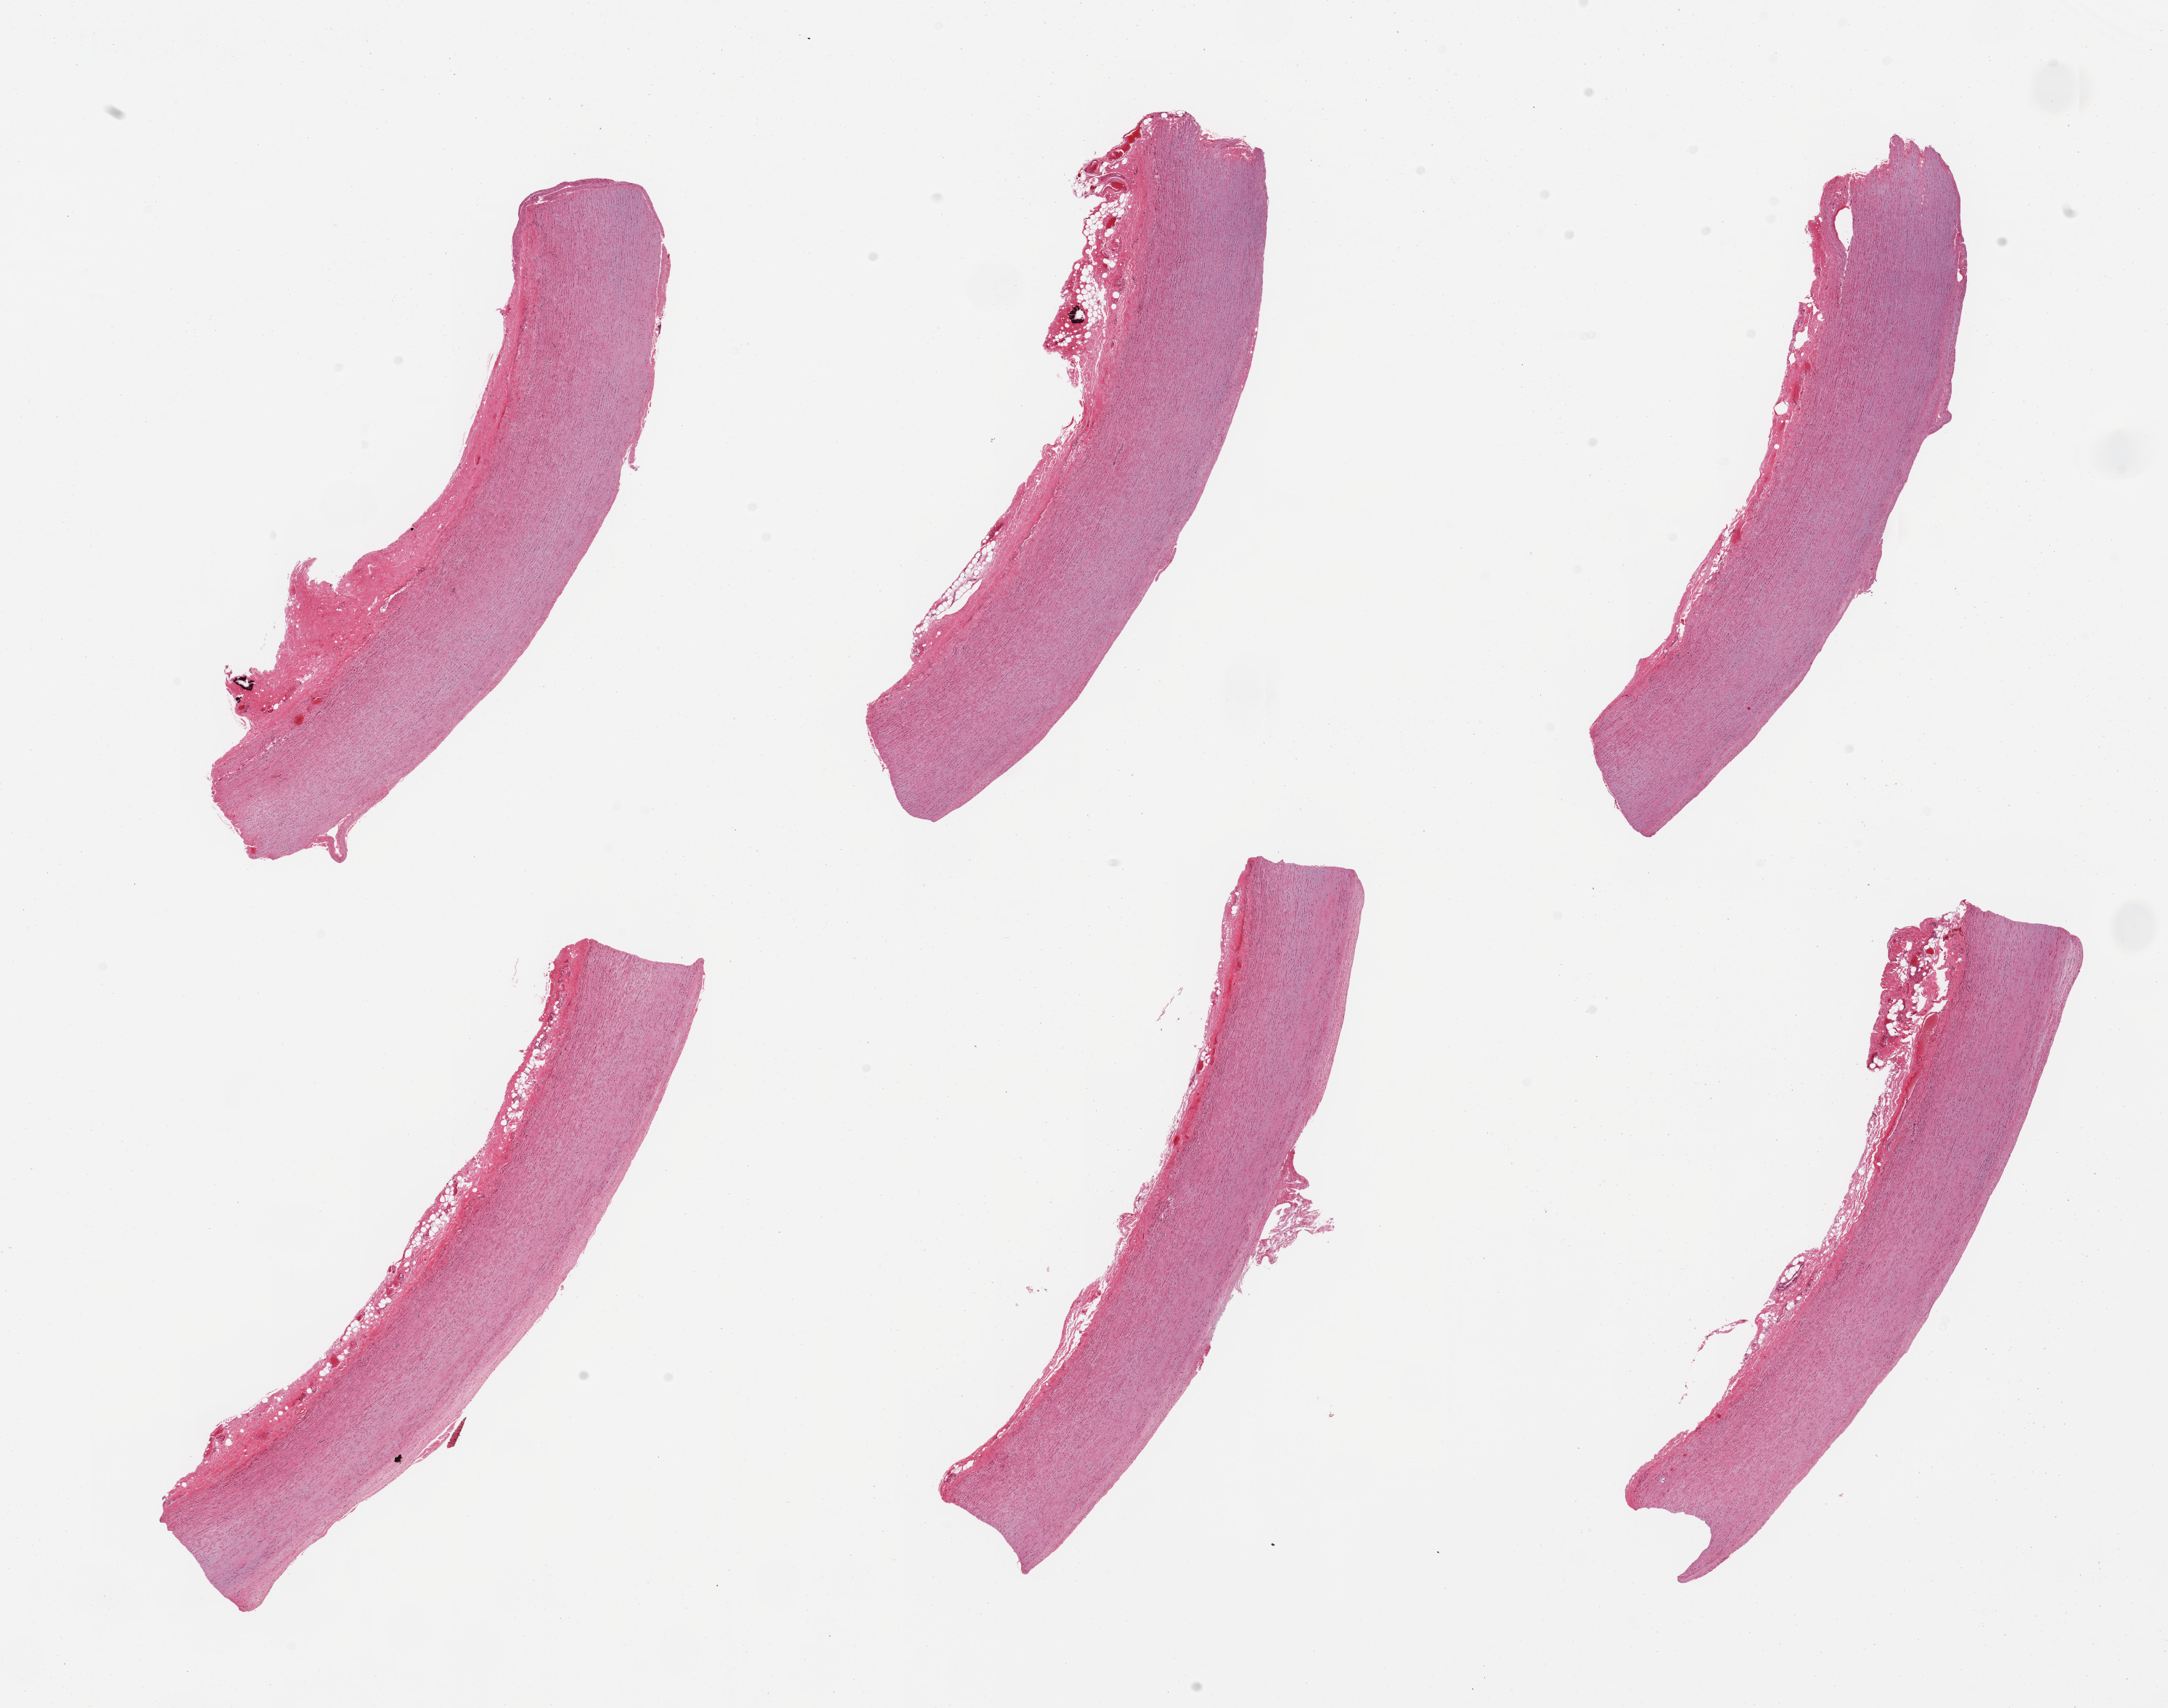
Hematoxylin and eosin (H&E) whole-slide image, low-resolution overview of the scanned area, about 23.6 x 18.6 mm. PAXgene-fixed, paraffin-embedded tissue. Section of aorta (target tissue). Donor tissue sample.
* pathologist's review note for this sample: 6 pieces, atheroisis (focal) up to ~0.25mm